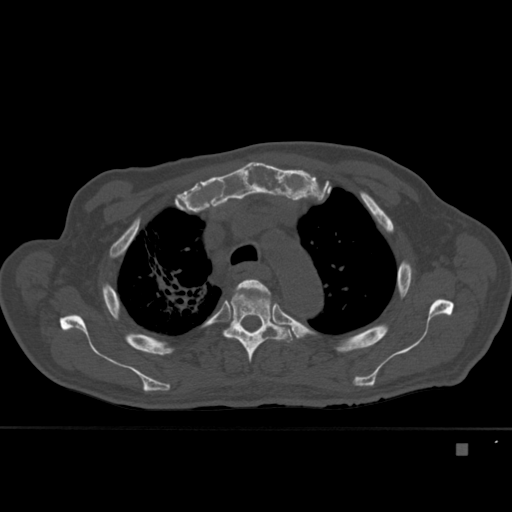
CT including the spine, one axial slice. Bone window (W 1800 / L 400 HU). 1.5 mm slice thickness. 512 × 512 image matrix, field of view 378 × 378 mm. Male patient, age 75 years. Case-level facts recorded for this patient, not image findings: primary cancer: prostate.
Structures marked on this image (semi-automatically segmented with operator editing):
- T3 vertebra: bounding box [x1, y1, x2, y2] px = [233, 279, 271, 299]
- T4 vertebra: [222, 284, 294, 362]